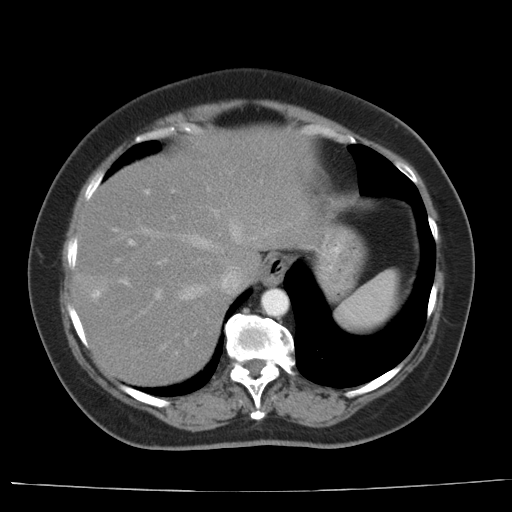
Contrast-enhanced abdominal CT, one axial slice; slice 29 of 44 in the series (ordered by position); 140 kVp; intravenous contrast given; soft-tissue window (W 400 / L 40 HU); 512 × 512 image matrix, field of view 373 × 373 mm. Female patient. From the clinical record (not read from this slice): diagnosis: colorectal cancer liver metastases, imaged before liver resection; multiple liver metastases: yes; largest metastasis: 1.8 cm; disease in both lobes: no.
Outlined on this slice (manually delineated by an expert):
- hepatic veins: bounding box <142,220,257,349> (left, top, right, bottom; pixels)
- liver: <72,128,324,387>
- planned liver remnant (the part of the liver to remain after resection): <103,128,324,279>
- portal vein (with intrahepatic branches): <114,187,209,353>